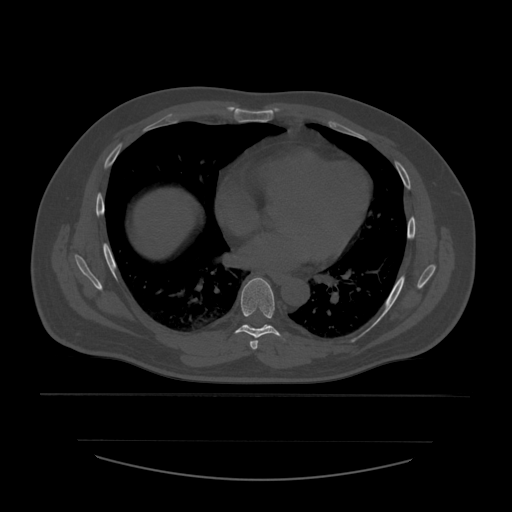
CT including the spine, one axial slice; position 359 of 532 along the scan axis; reconstruction kernel STANDARD; 120 kVp; bone window (W 1800 / L 400 HU); 1.25 mm slice thickness; 512 × 512 image matrix, field of view 441 × 441 mm. Patient age 44 years. Case-level facts recorded for this patient, not image findings: primary cancer: soft tissue sarcoma.
Outlined on this slice (semi-automatic segmentation, software-assisted and operator-edited):
- T6 vertebra: box from (x=250, y=341) to (x=259, y=350) px
- T7 vertebra: (x=235, y=278)–(x=281, y=338)